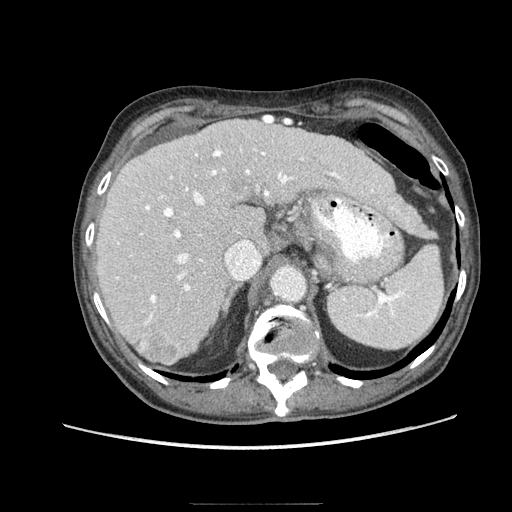
Contrast-enhanced abdominal CT (liver protocol), one axial slice; 140 kVp; soft-tissue window (W 400 / L 40 HU); 2.5 mm slice thickness; 512 × 512 image matrix, field of view 360 × 360 mm. From the clinical record (not read from this slice): diagnosis: hepatocellular carcinoma (patient treated with transarterial chemoembolisation; whether this scan precedes or follows treatment is not stated here); TNM stage (as recorded): Stage-I; Child-Pugh class: A; tumour nodularity: uninodular.
Outlined on this slice (semi-automatically segmented with operator editing):
- liver parenchyma outside the tumour (the mass and vessels are separate outlines, so this box may not span the whole liver): bounding box <96,118,409,362> (left, top, right, bottom; pixels)
- mass: <138,330,180,366>
- liver vessels: <116,116,398,325>